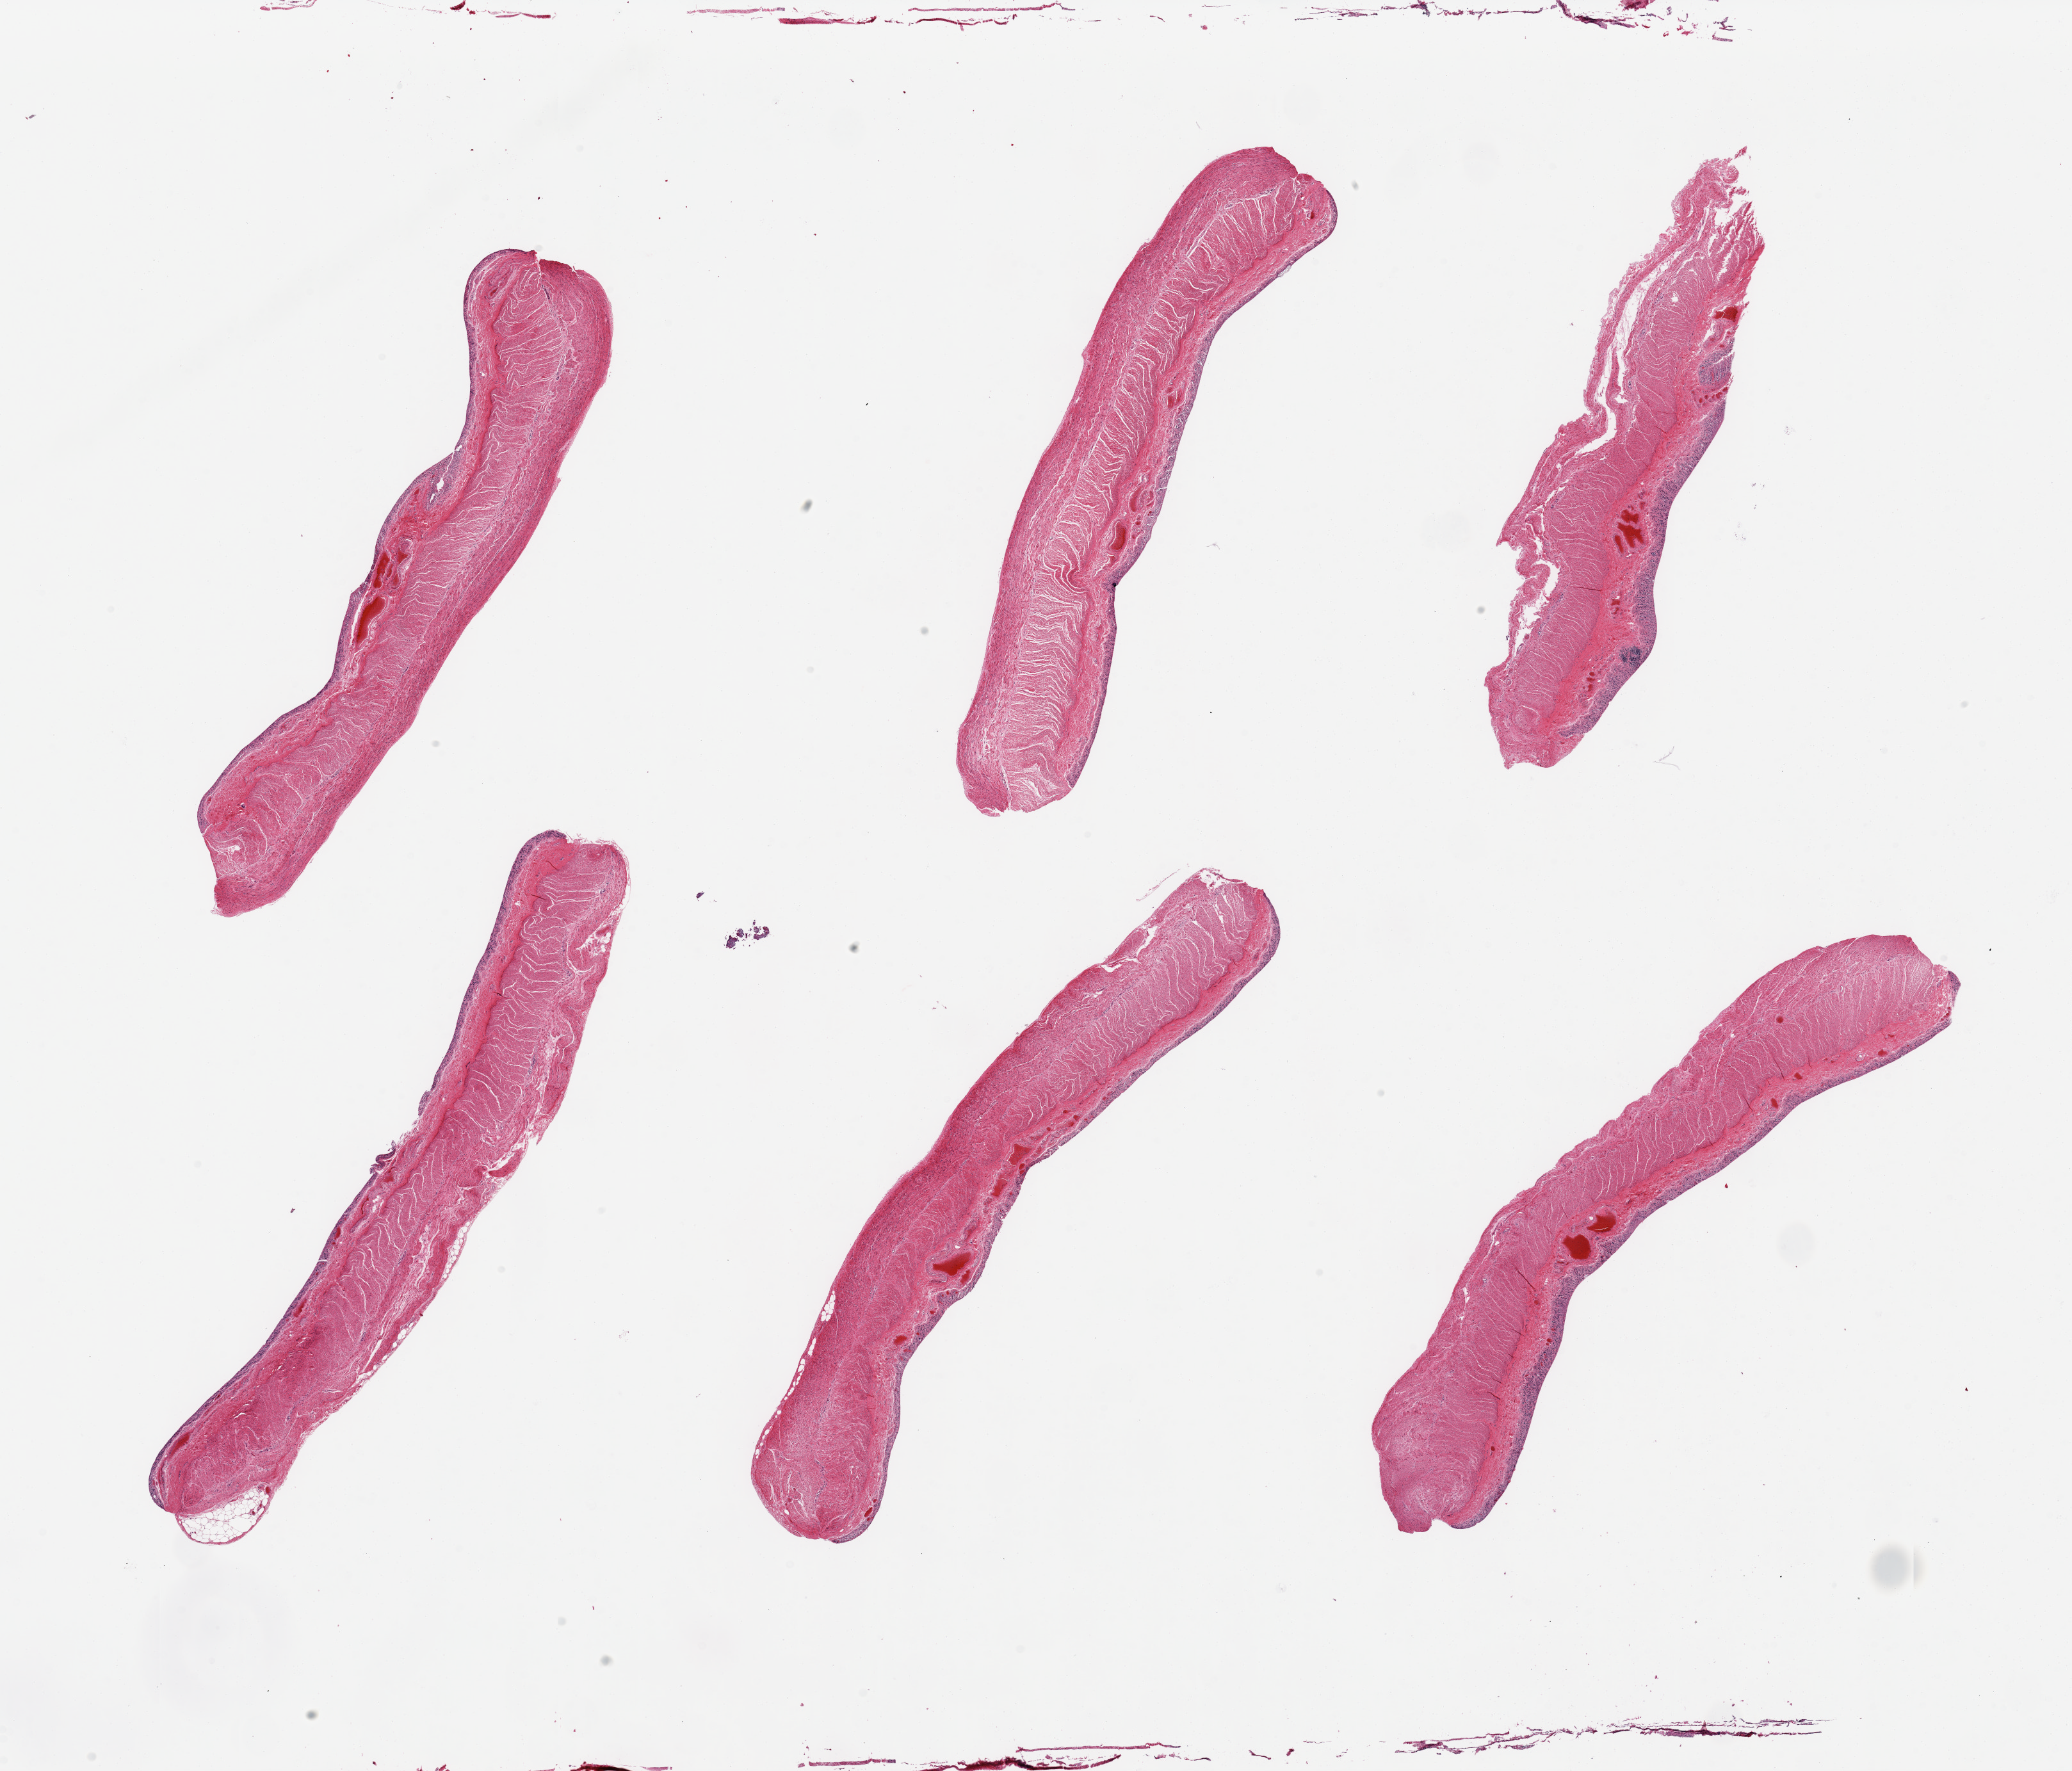
Digitized hematoxylin and eosin (H&E)-stained section, shown as a low-resolution overview of the whole scanned area (about 25.6 x 21.9 mm, from a 20x scan). PAXgene-fixed, paraffin-embedded tissue. Sampled site (target tissue): transverse colon. Tissue donor sample.
* reviewer comment on this tissue sample: 6 pieces; mucosa totaly autolyzed, muscularis intact